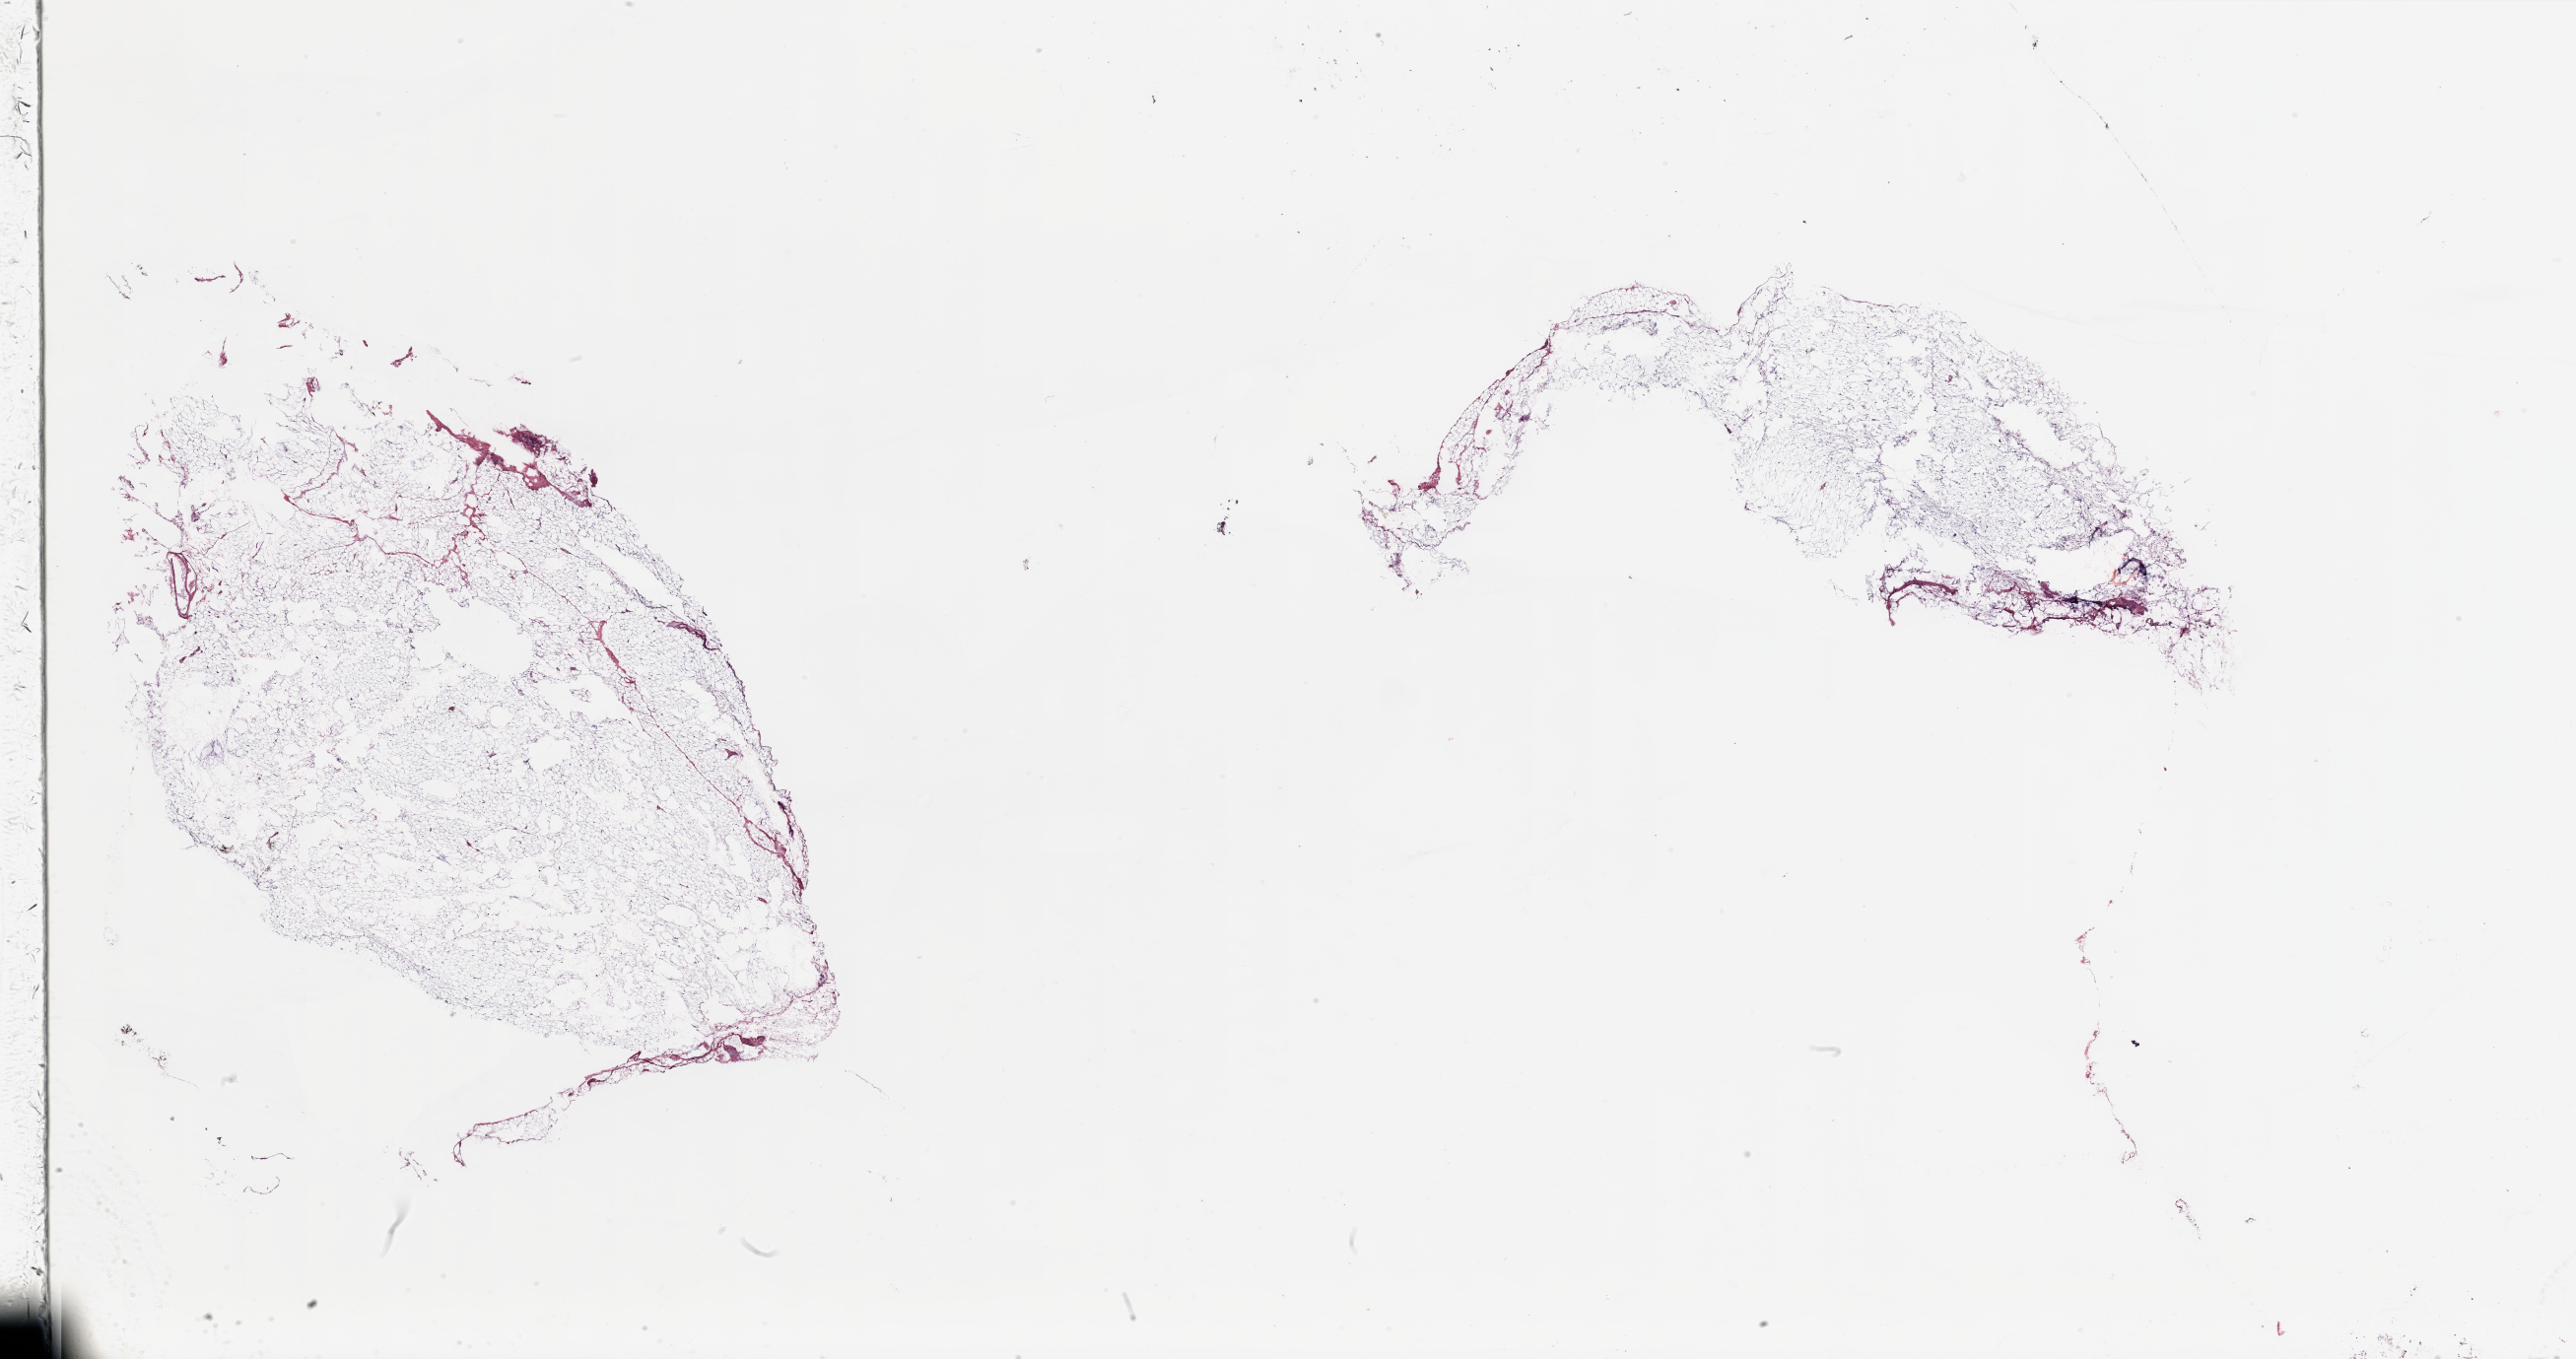
Digitized Hematoxylin and eosin (H&E) stained tissue section (whole slide) — low-resolution overview of the scanned area, about 41.3 x 21.8 mm; tumour tissue sample, breast. Patient: female, age 58 years.
- histologic diagnosis: Infiltrating duct carcinoma, NOS
- AJCC pathologic stage: IIA